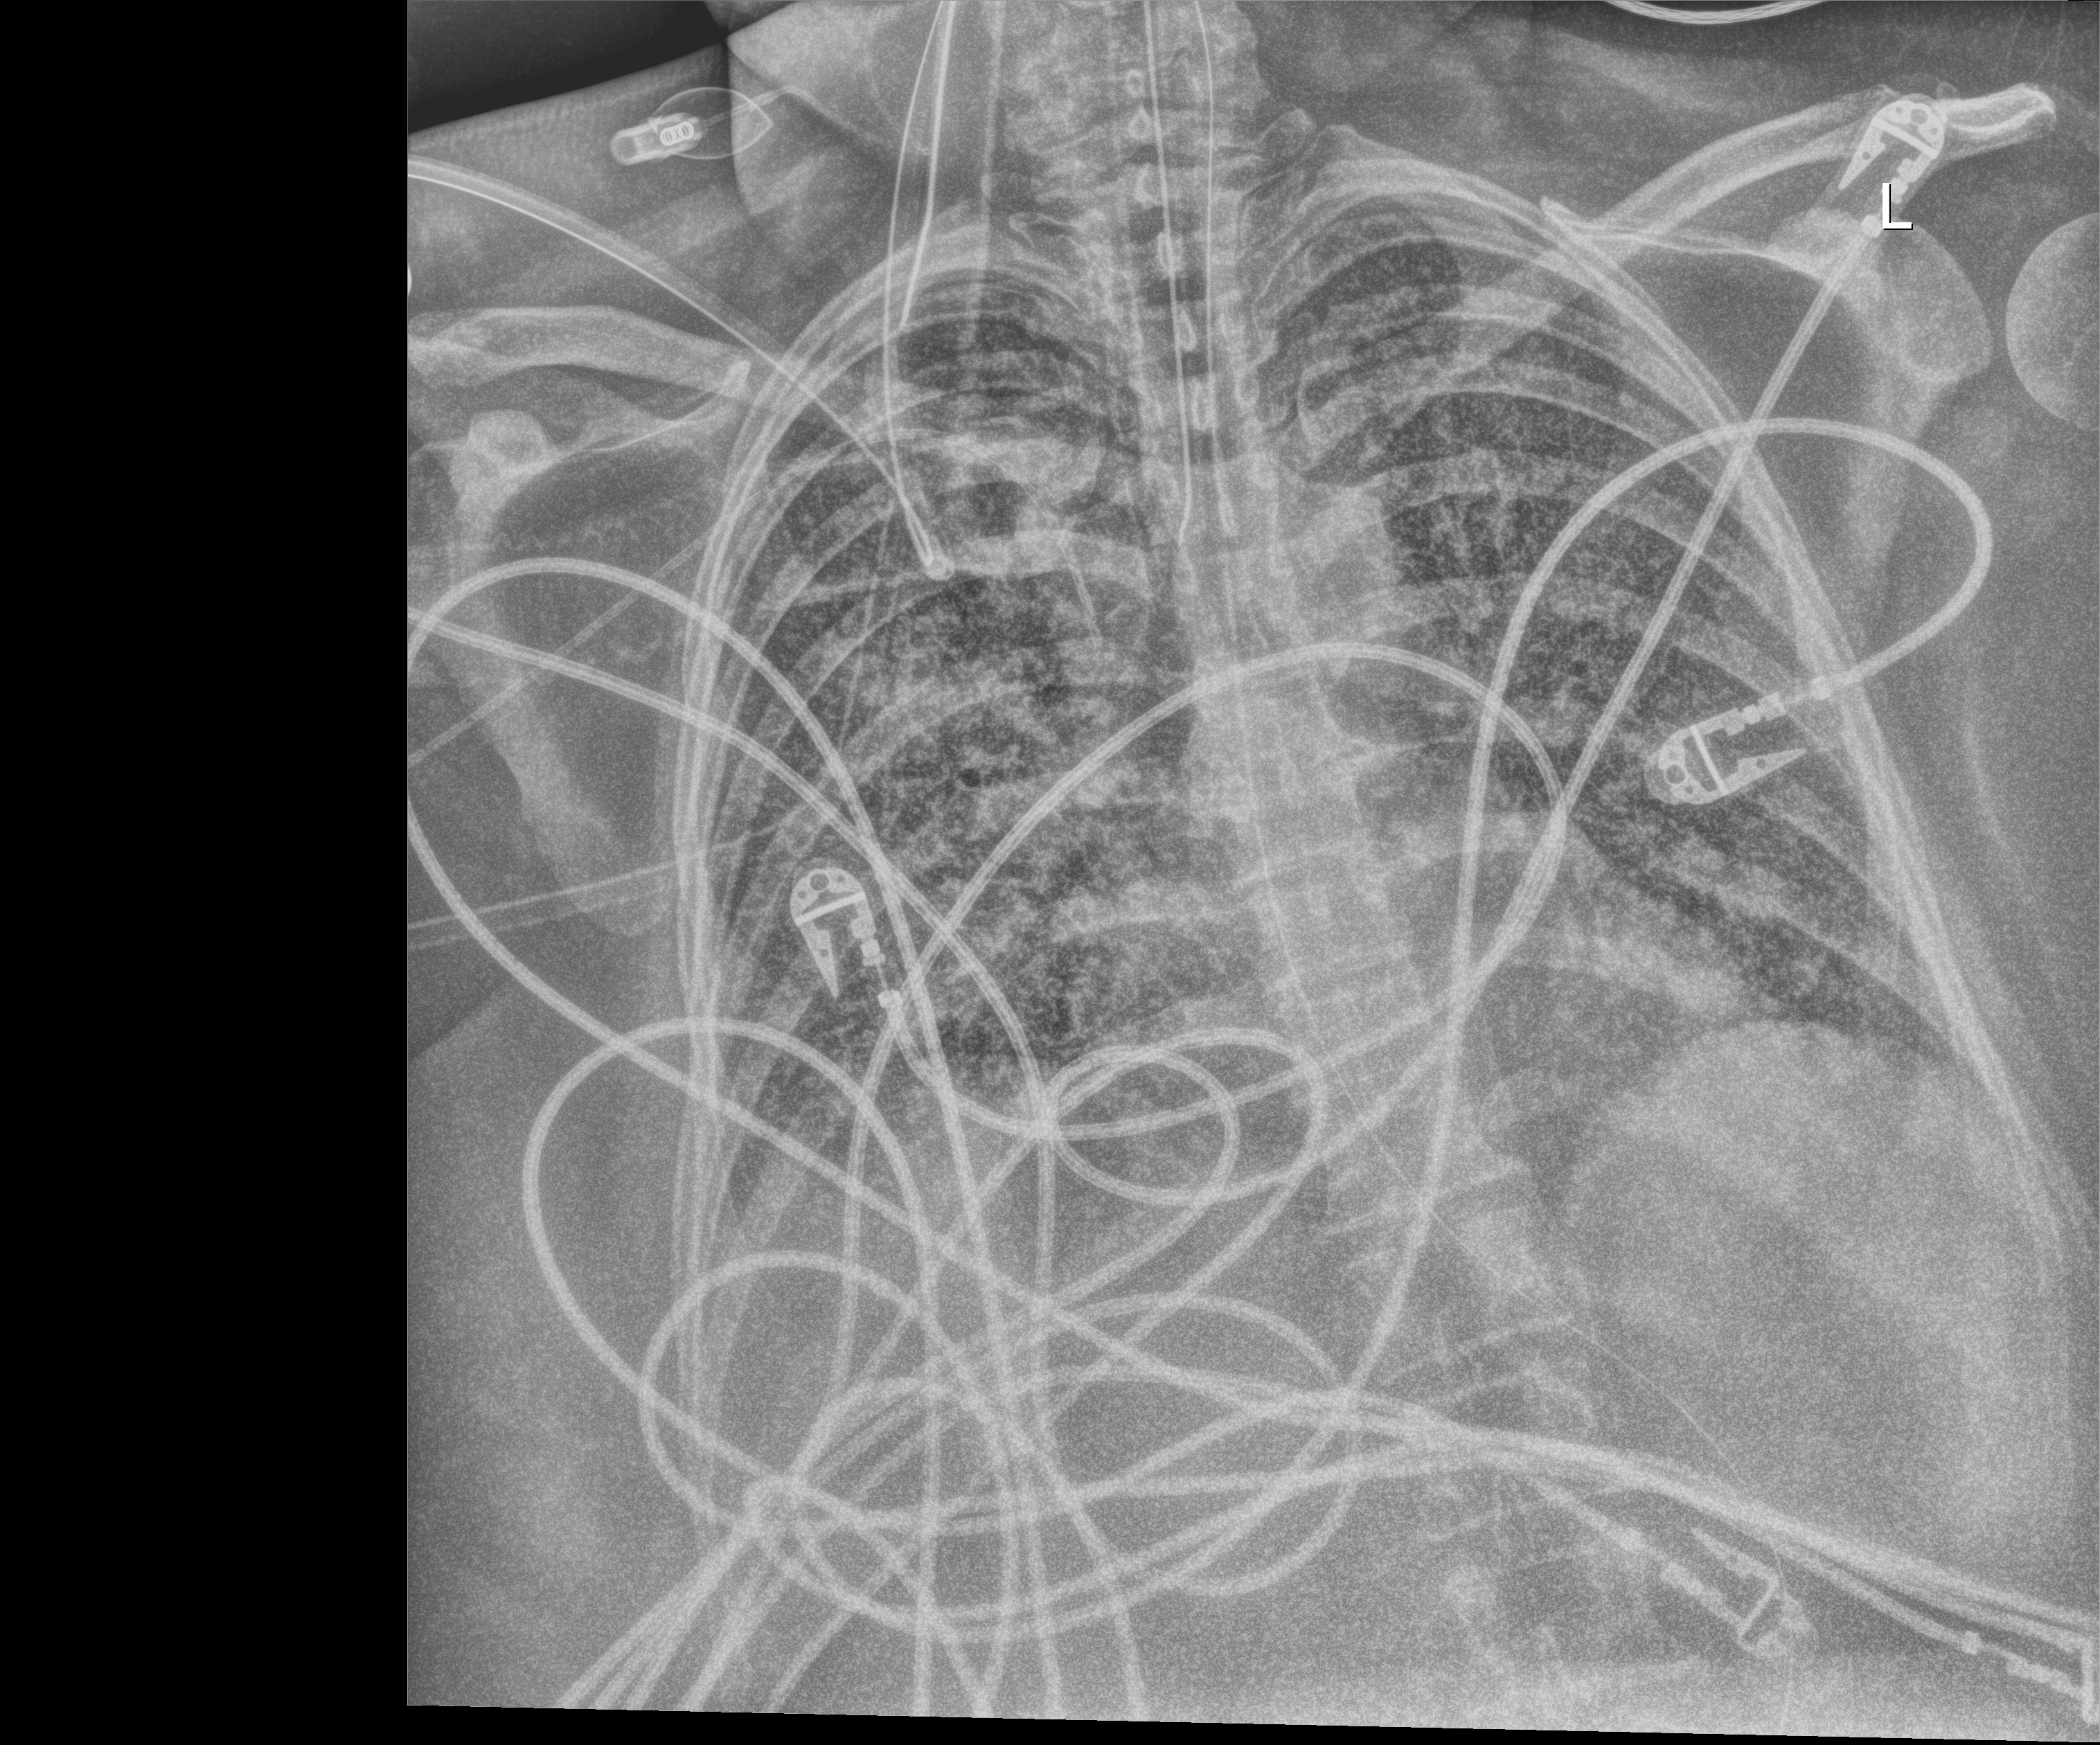
Portable chest radiograph, anteroposterior (AP) projection. Female patient hospitalised with COVID-19, age 18–59 years.
Hospital-stay facts (about this admission, not read from this image; timing relative to this image not recorded):
- admitted to intensive care during this hospital stay: yes
- mechanically ventilated during this hospital stay: yes